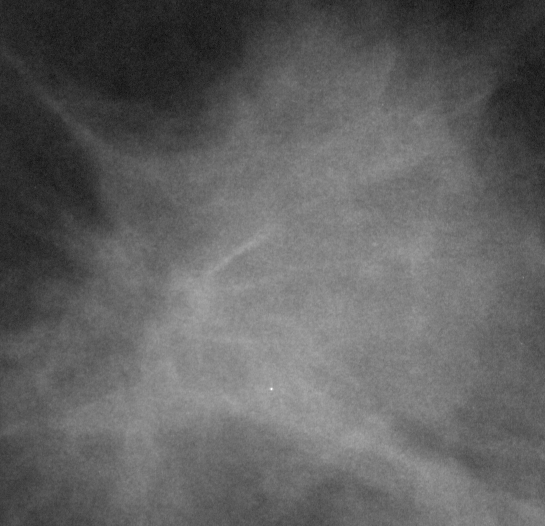
Crop from a digitized film mammogram around one marked abnormality, right breast, MLO view, BI-RADS breast density category 3 (scale 1–4).
Marked abnormality: mass, shape irregular, margins spiculated; BI-RADS assessment category 5; pathology (as recorded): malignant.